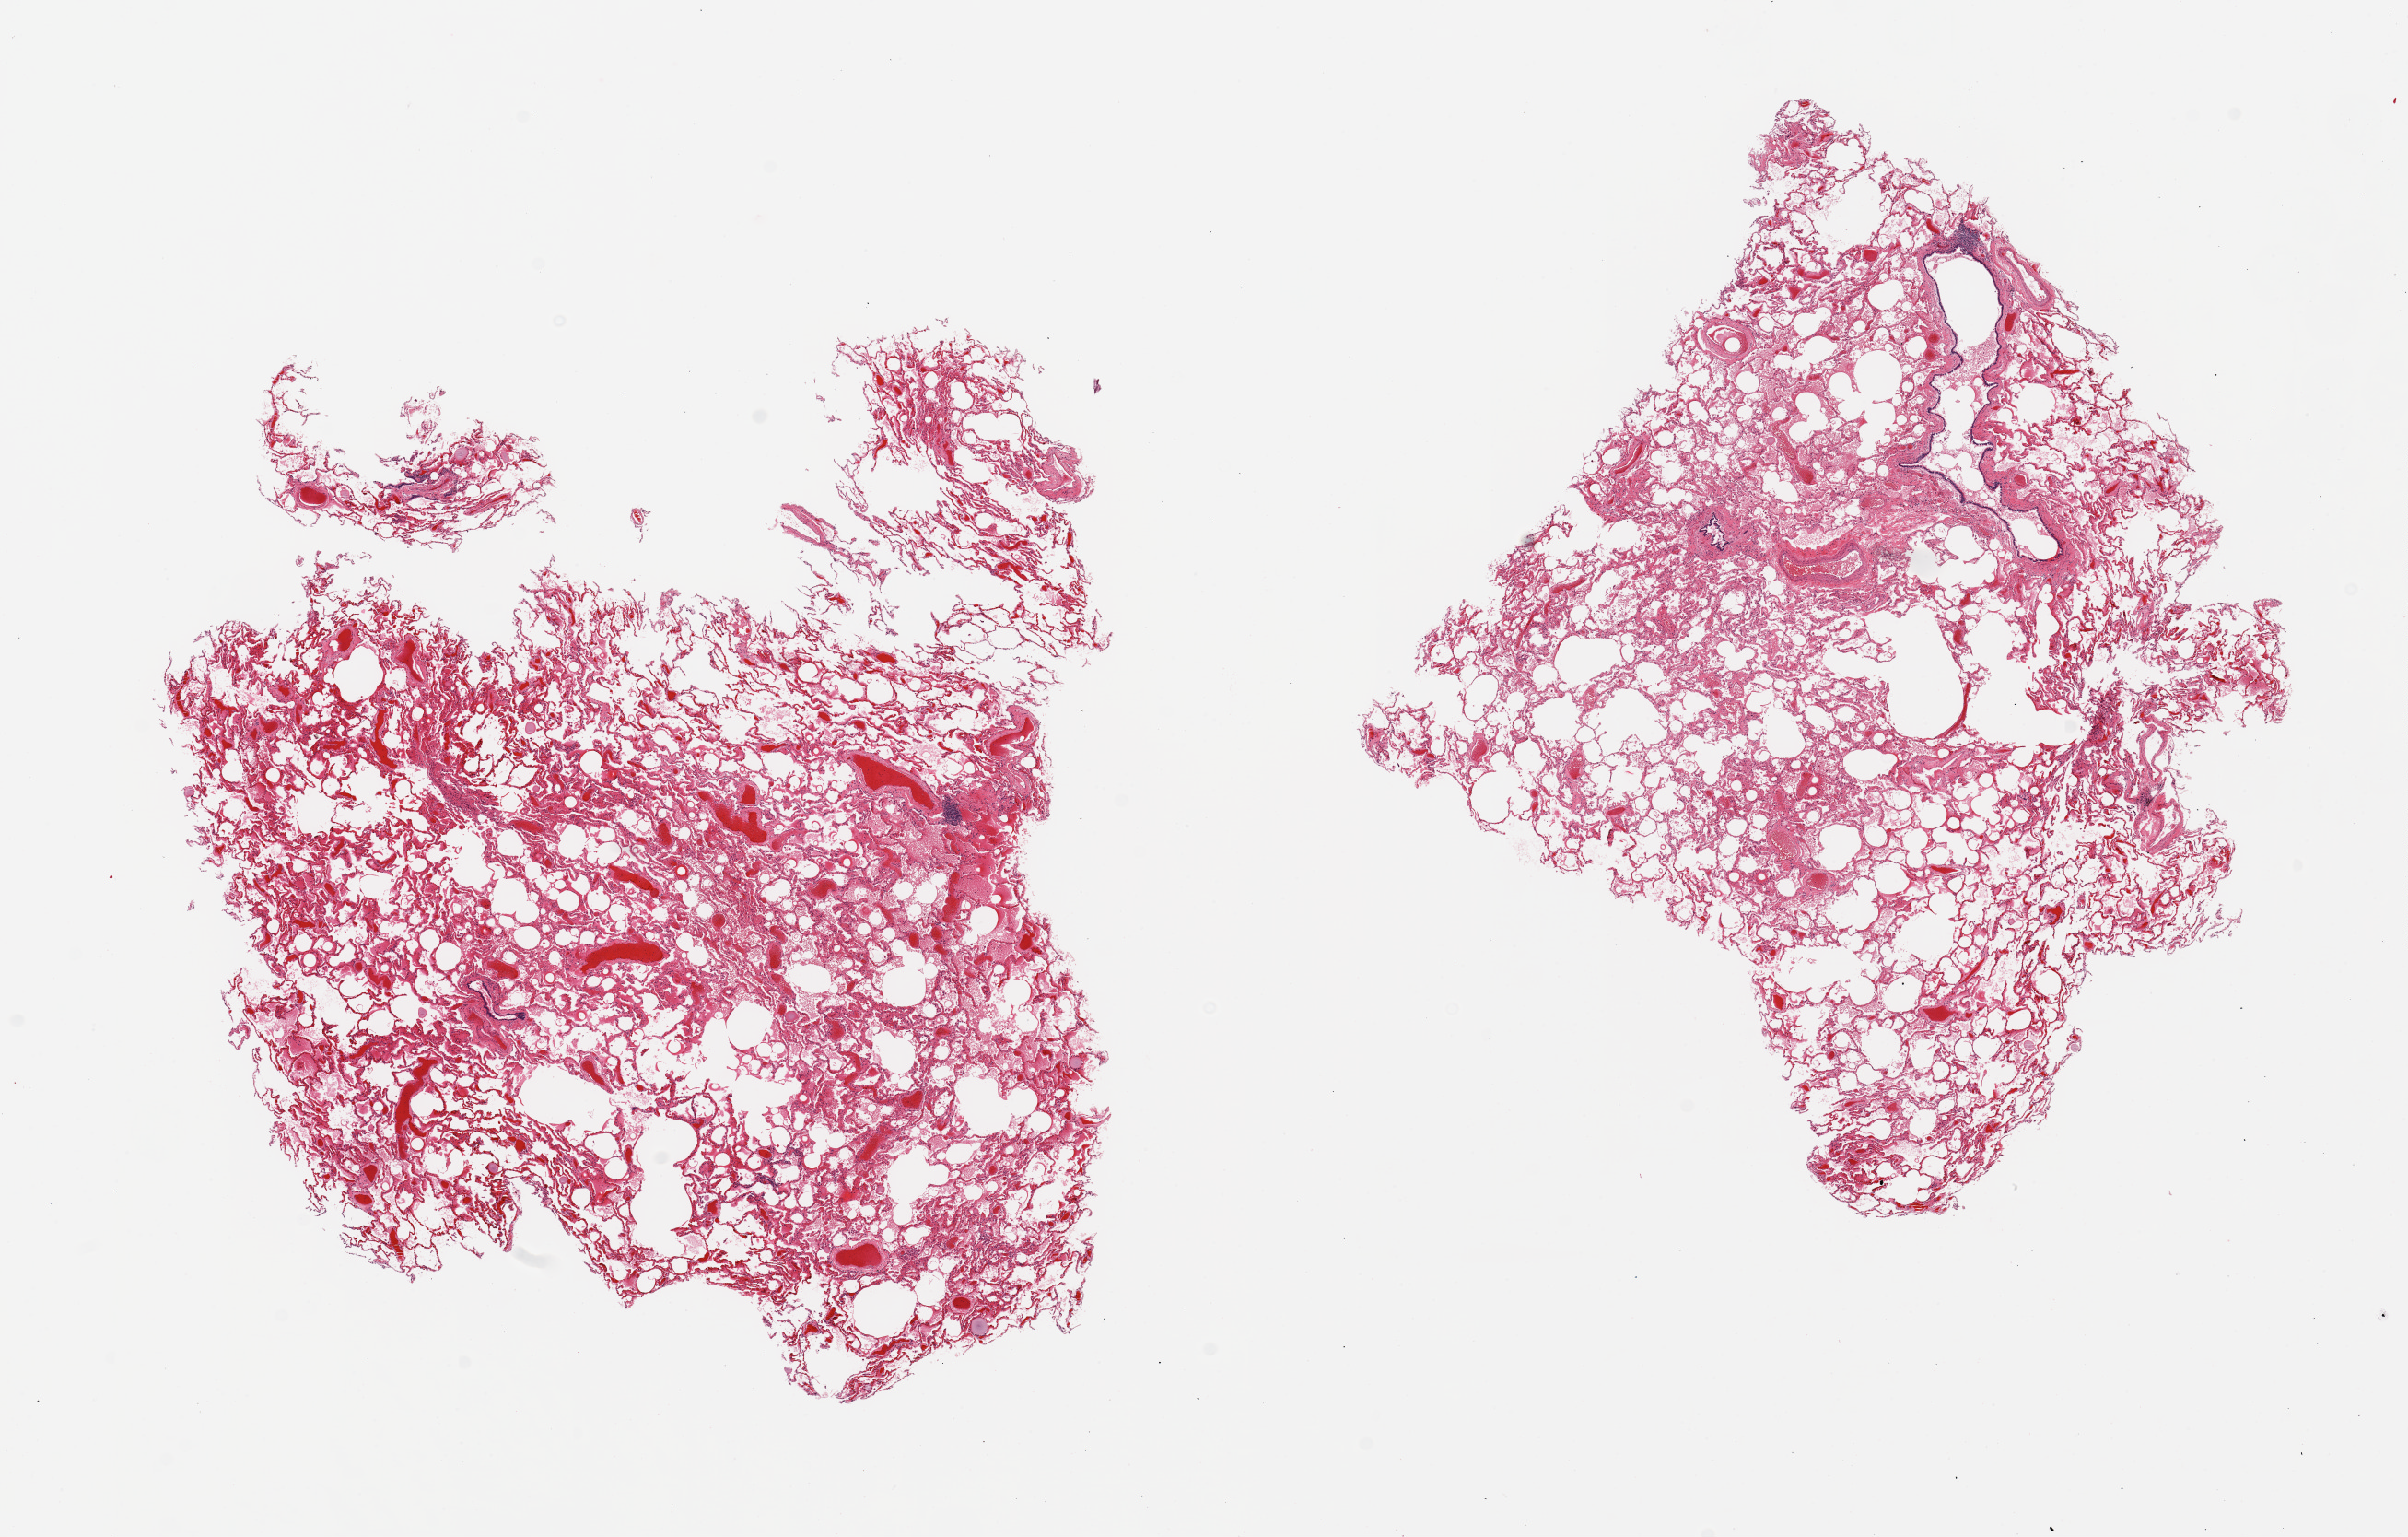
Digitized haematoxylin and eosin-stained section, brightfield, low-resolution overview of the scanned area, about 20.7 x 13.2 mm (slide scanned at 20x), PAXgene-fixed paraffin-embedded (PFPE) section, sampled site (target tissue): lung, tissue donor sample. Female donor.
• review note (as recorded): 2 pieces; congestion and emphysematous changes